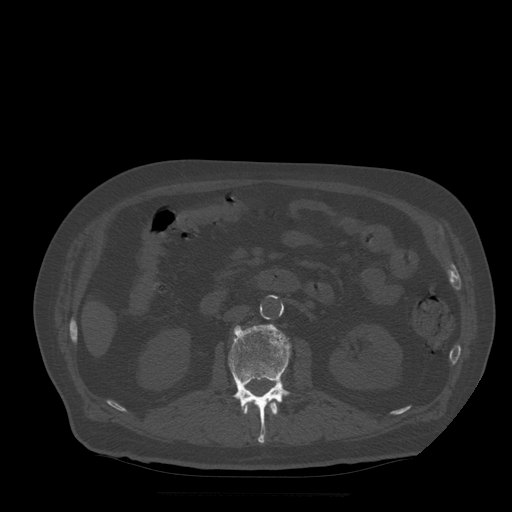
CT including the spine, one axial slice; slice 168 of 522 in the series (ordered by position); bone window (W 1800 / L 400 HU); 1.25 mm slice thickness; 512 × 512 image matrix. Patient age 72 years. Case-level facts recorded for this patient, not image findings: primary cancer: prostate.
Structures marked on this image (semi-automatic segmentation, software-assisted and operator-edited):
- L1 vertebra: bounding box (x1, y1, x2, y2) in pixels: (245, 402, 278, 416)
- L2 vertebra: (229, 325, 291, 443)